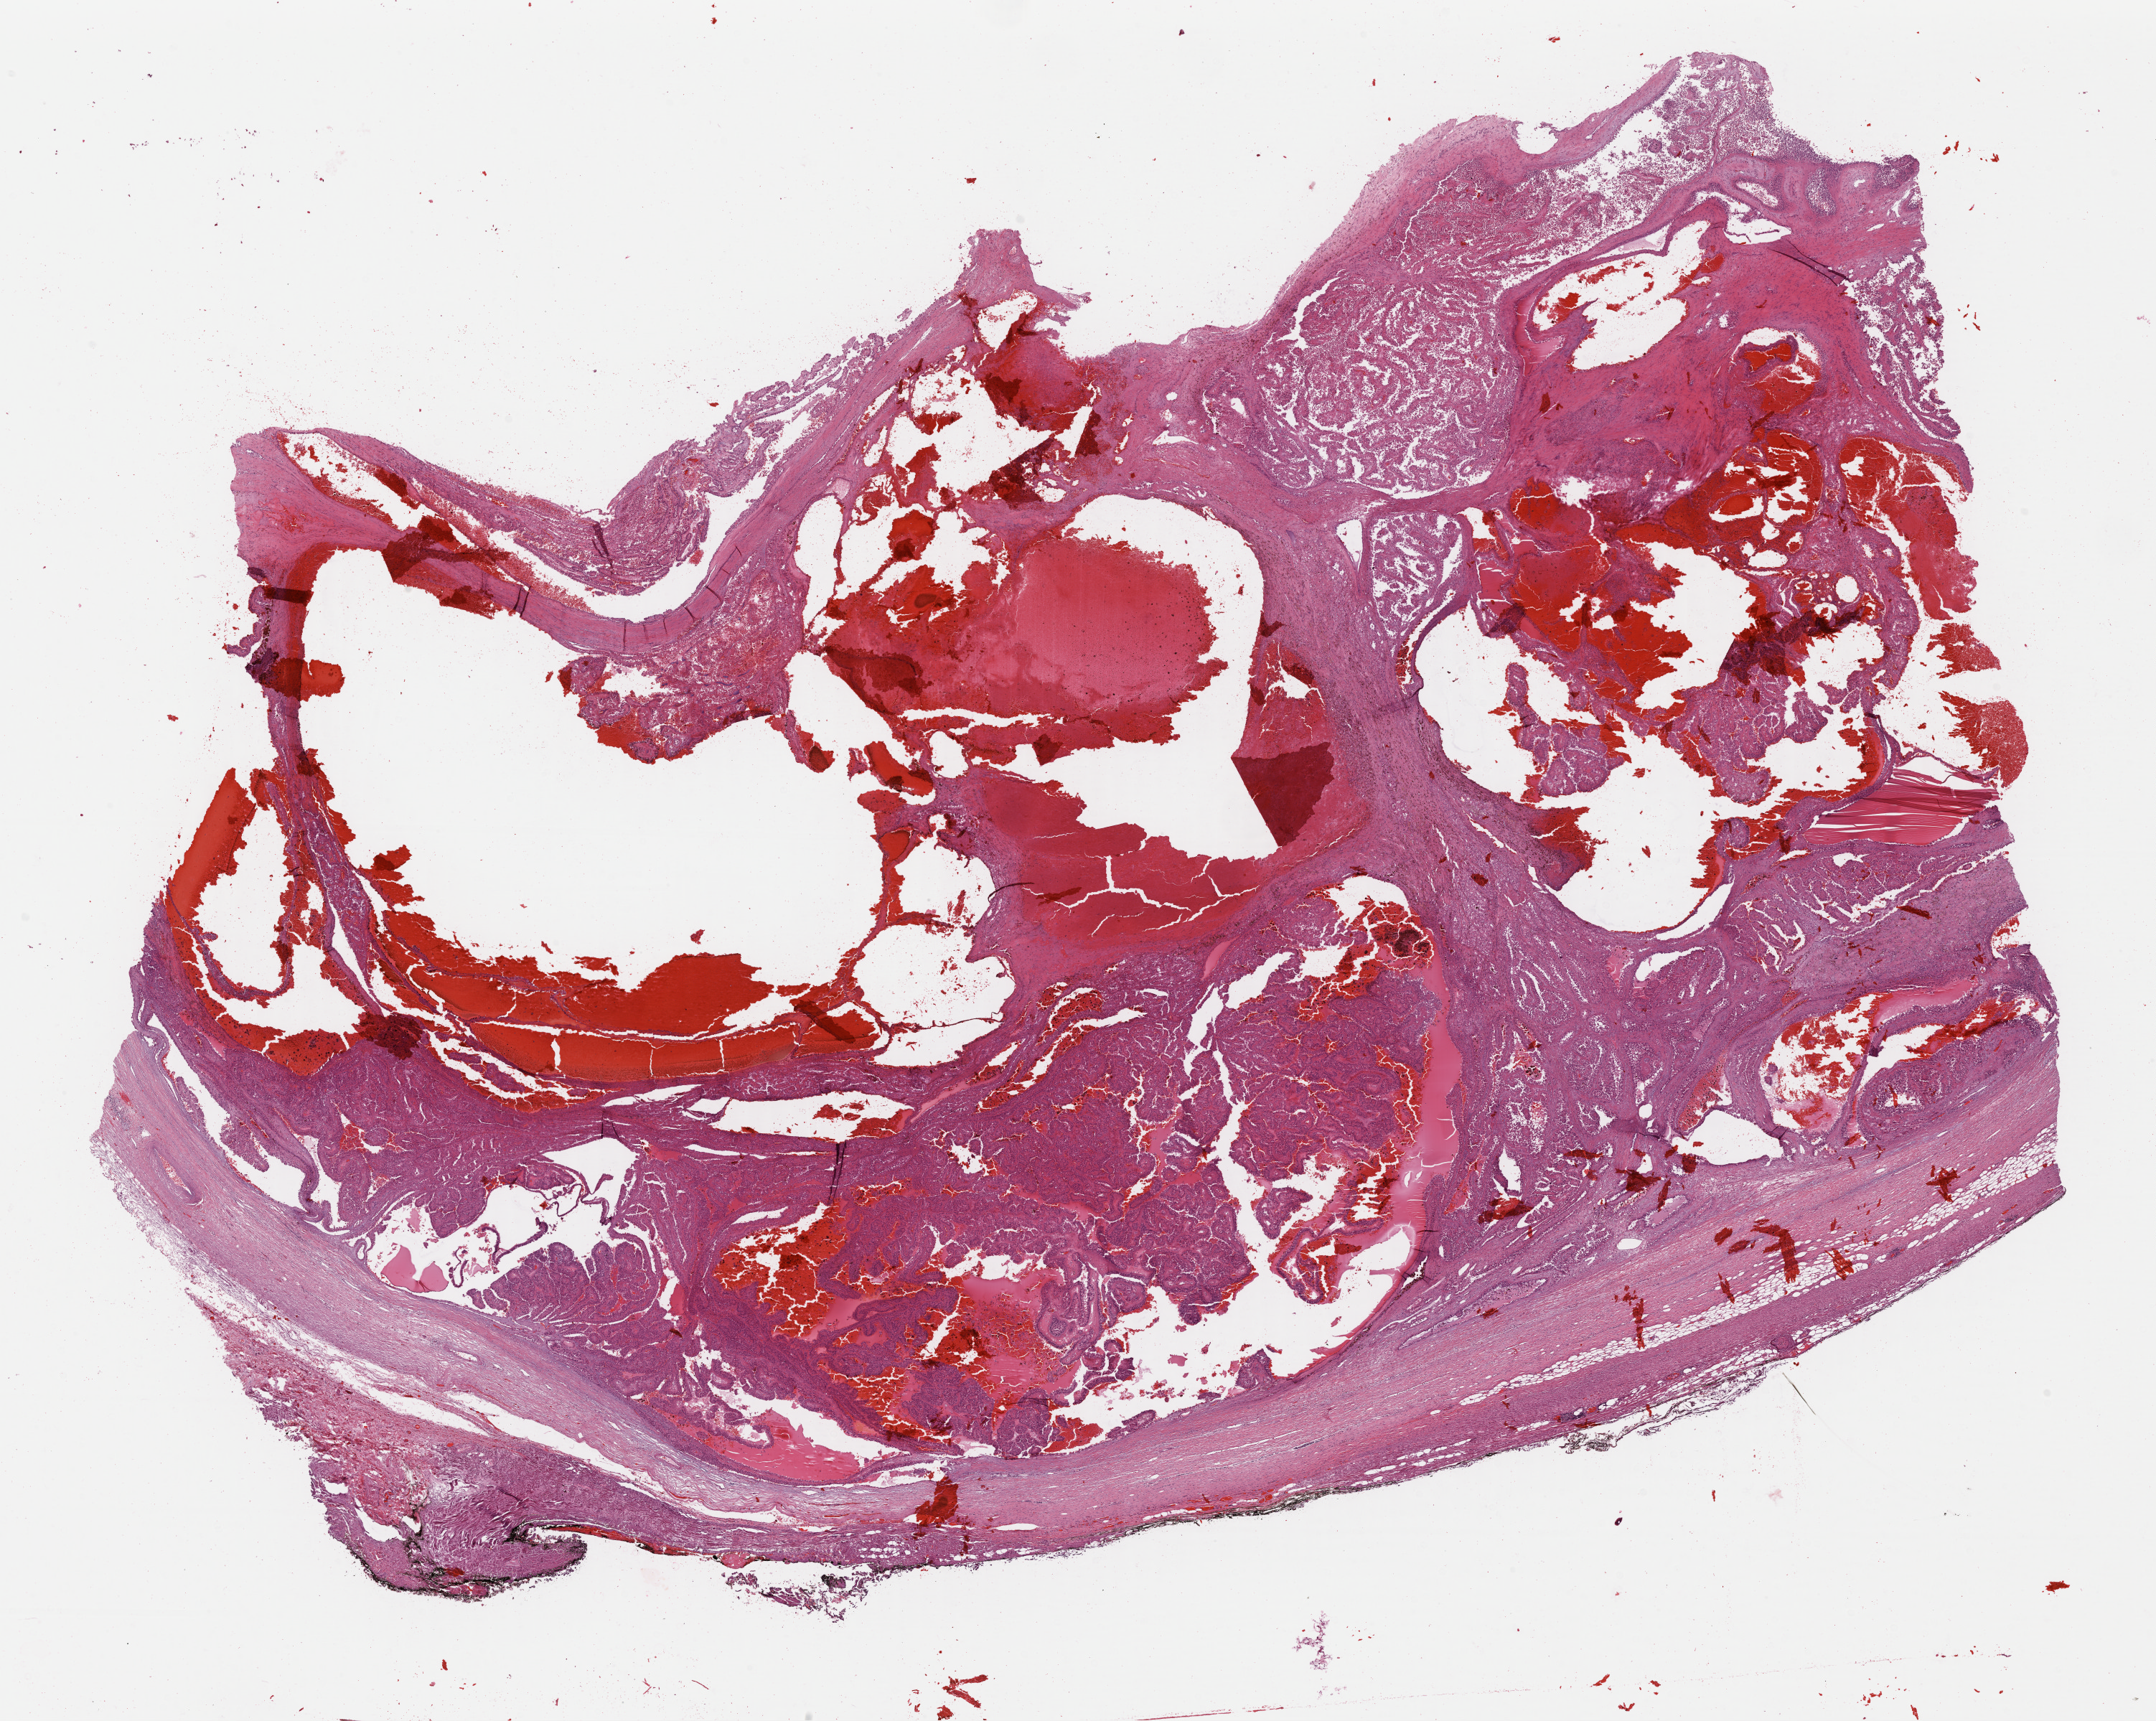
Whole-slide histology image, H&E-stained, whole scanned area (about 23.6 x 18.9 mm) shown as a low-resolution overview; formalin-fixed paraffin-embedded (FFPE) diagnostic section; kidney, primary tumour sample. Patient: male, age at initial diagnosis 82 years.
Histologic diagnosis: Papillary adenocarcinoma, NOS.